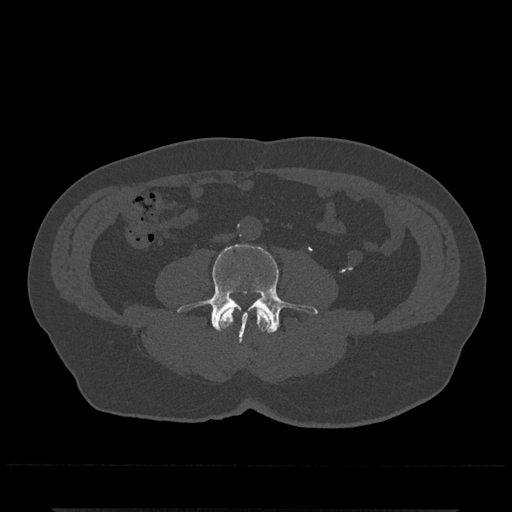
CT including the spine, one axial slice. Reconstruction kernel Br40s/3. 120 kVp. Bone window (W 1800 / L 400 HU). 0.5 mm slice thickness. 512 × 512 image matrix, field of view 393 × 393 mm. Male patient, age 67 years. Case-level facts recorded for this patient, not image findings: primary cancer: prostate.
Structures marked on this image (semi-automatic segmentation, software-assisted and operator-edited):
- L3 vertebra: bounding box [x1, y1, x2, y2] px = [219, 305, 272, 332]
- L4 vertebra: [177, 244, 318, 341]